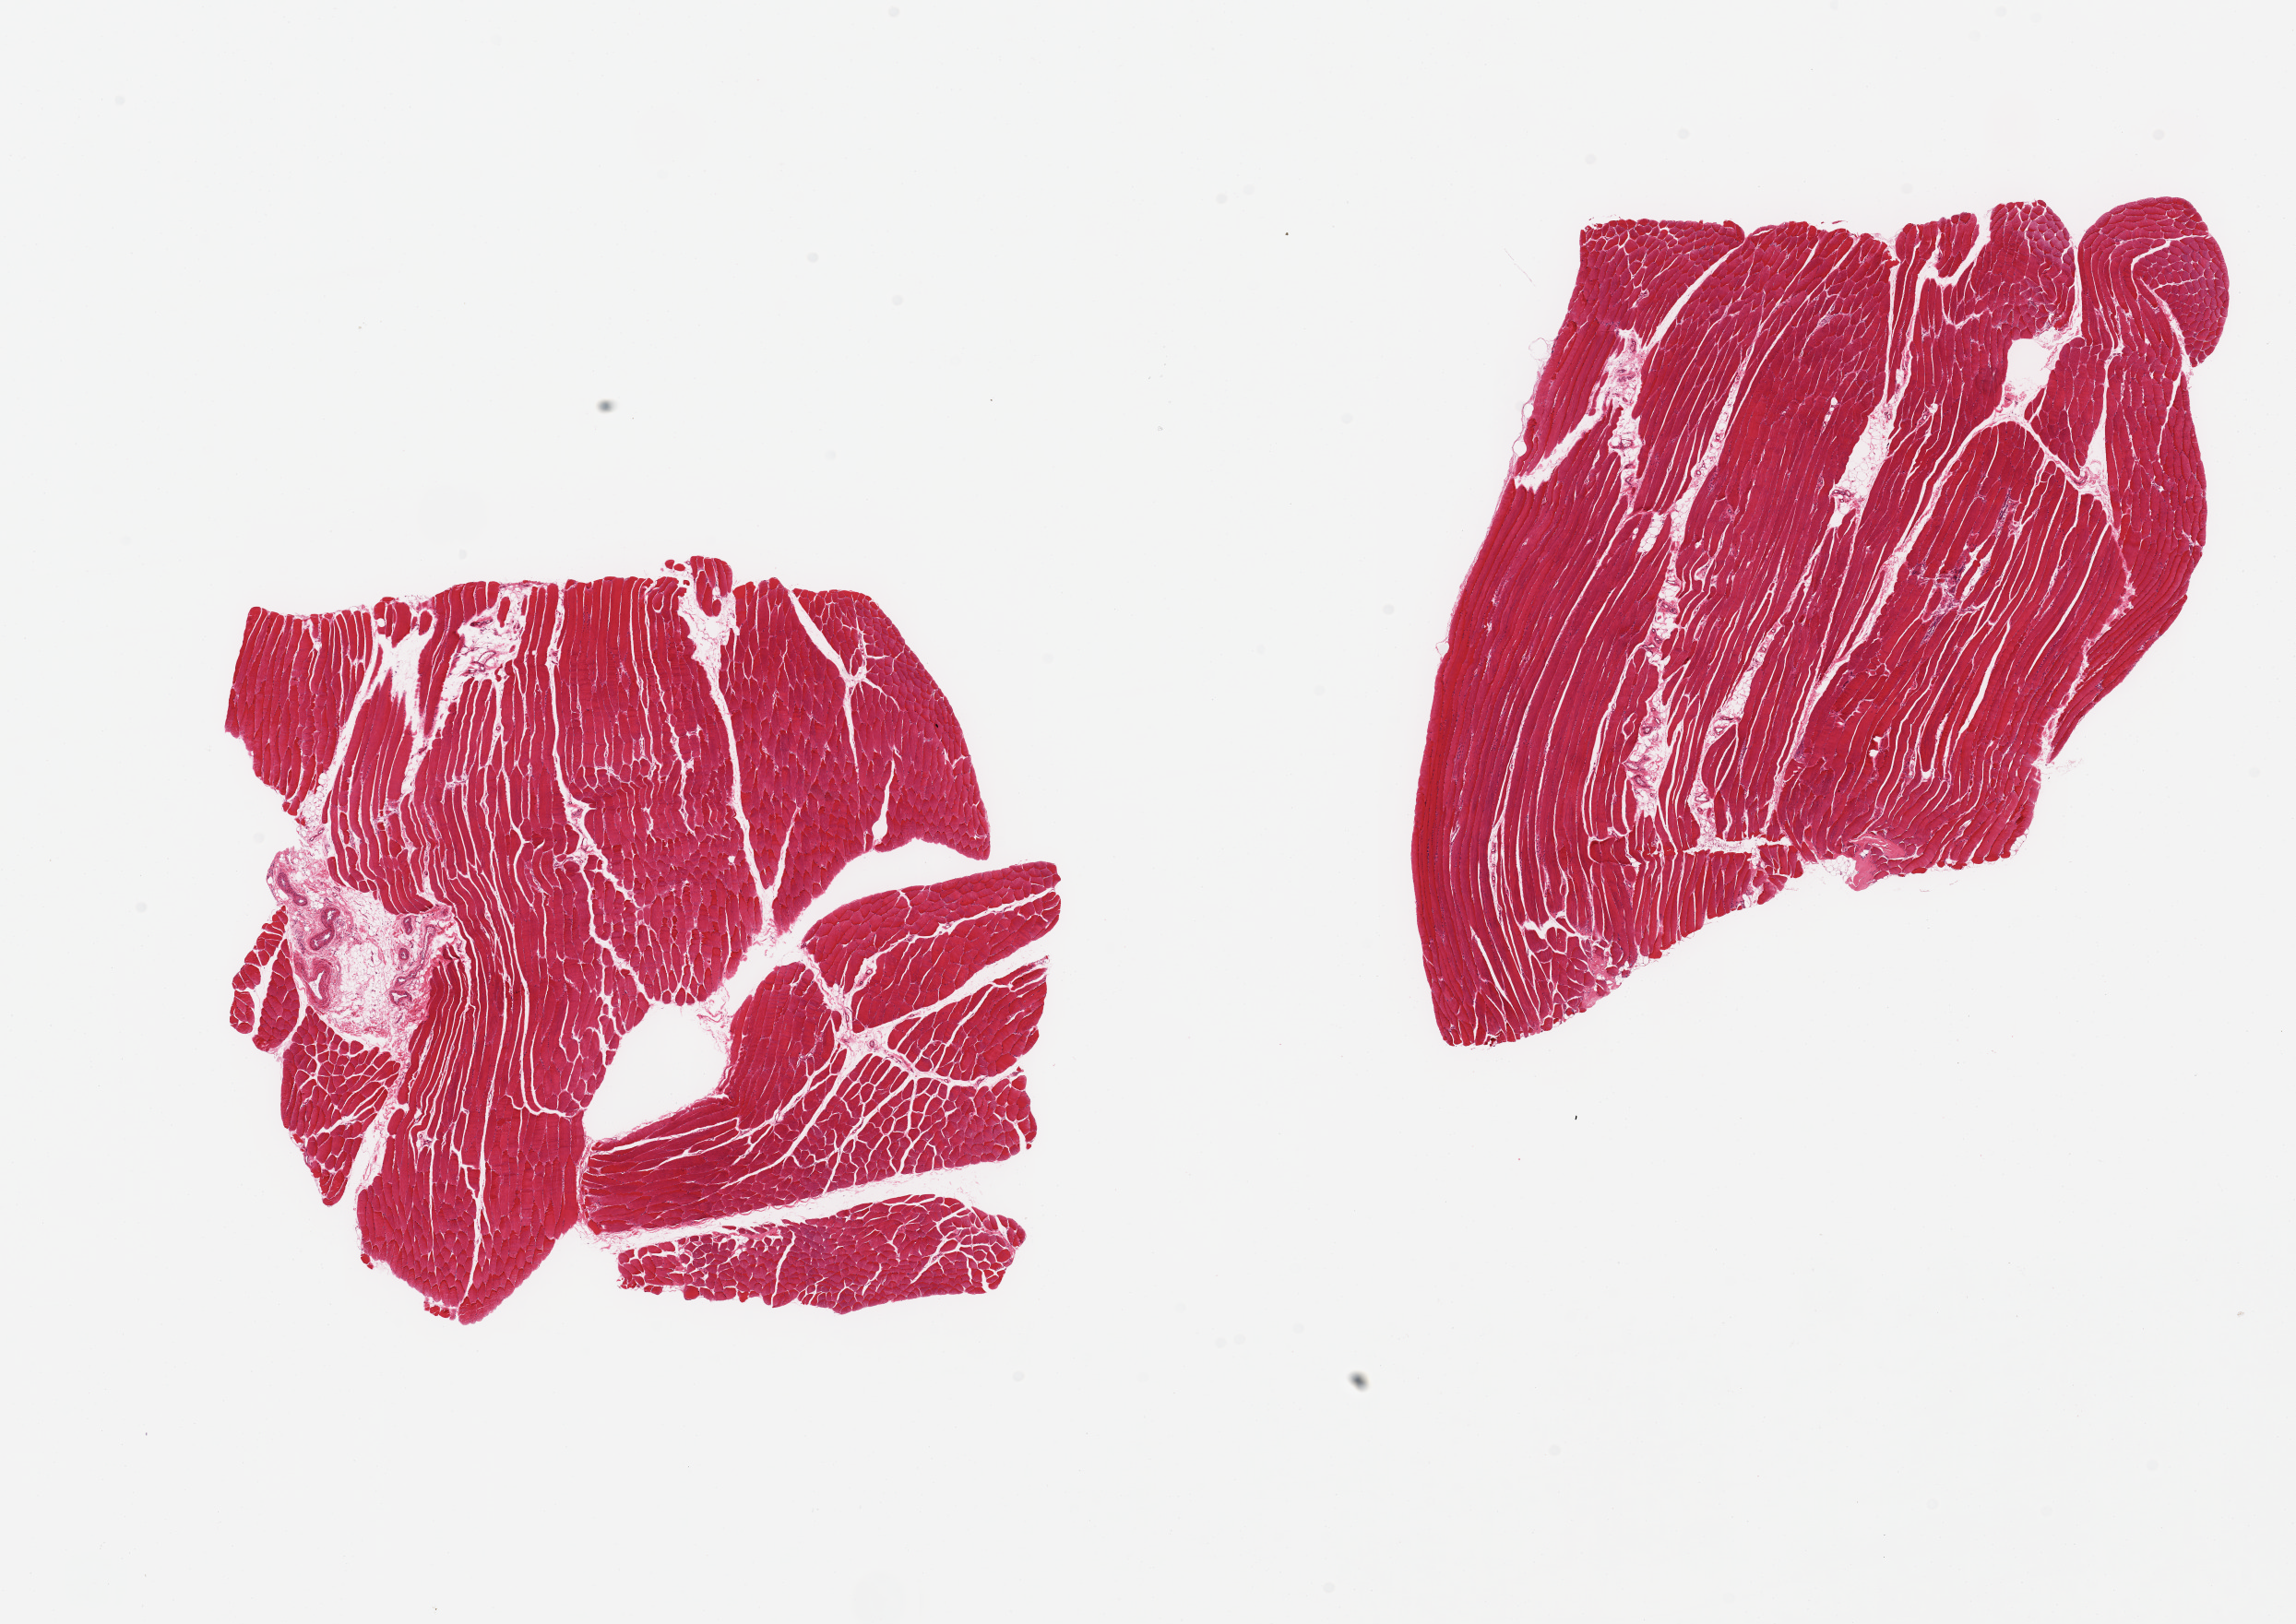
Whole-slide image, haematoxylin and eosin stain, low-resolution overview of the scanned area, about 19.7 x 13.9 mm (acquisition: 20x scan), PAXgene-fixed paraffin-embedded (PFPE) section, sampled site (target tissue): skeletal muscle, donor tissue sample.
Pathologist's review note for this sample: 2 pieces; 10% internal fat content.